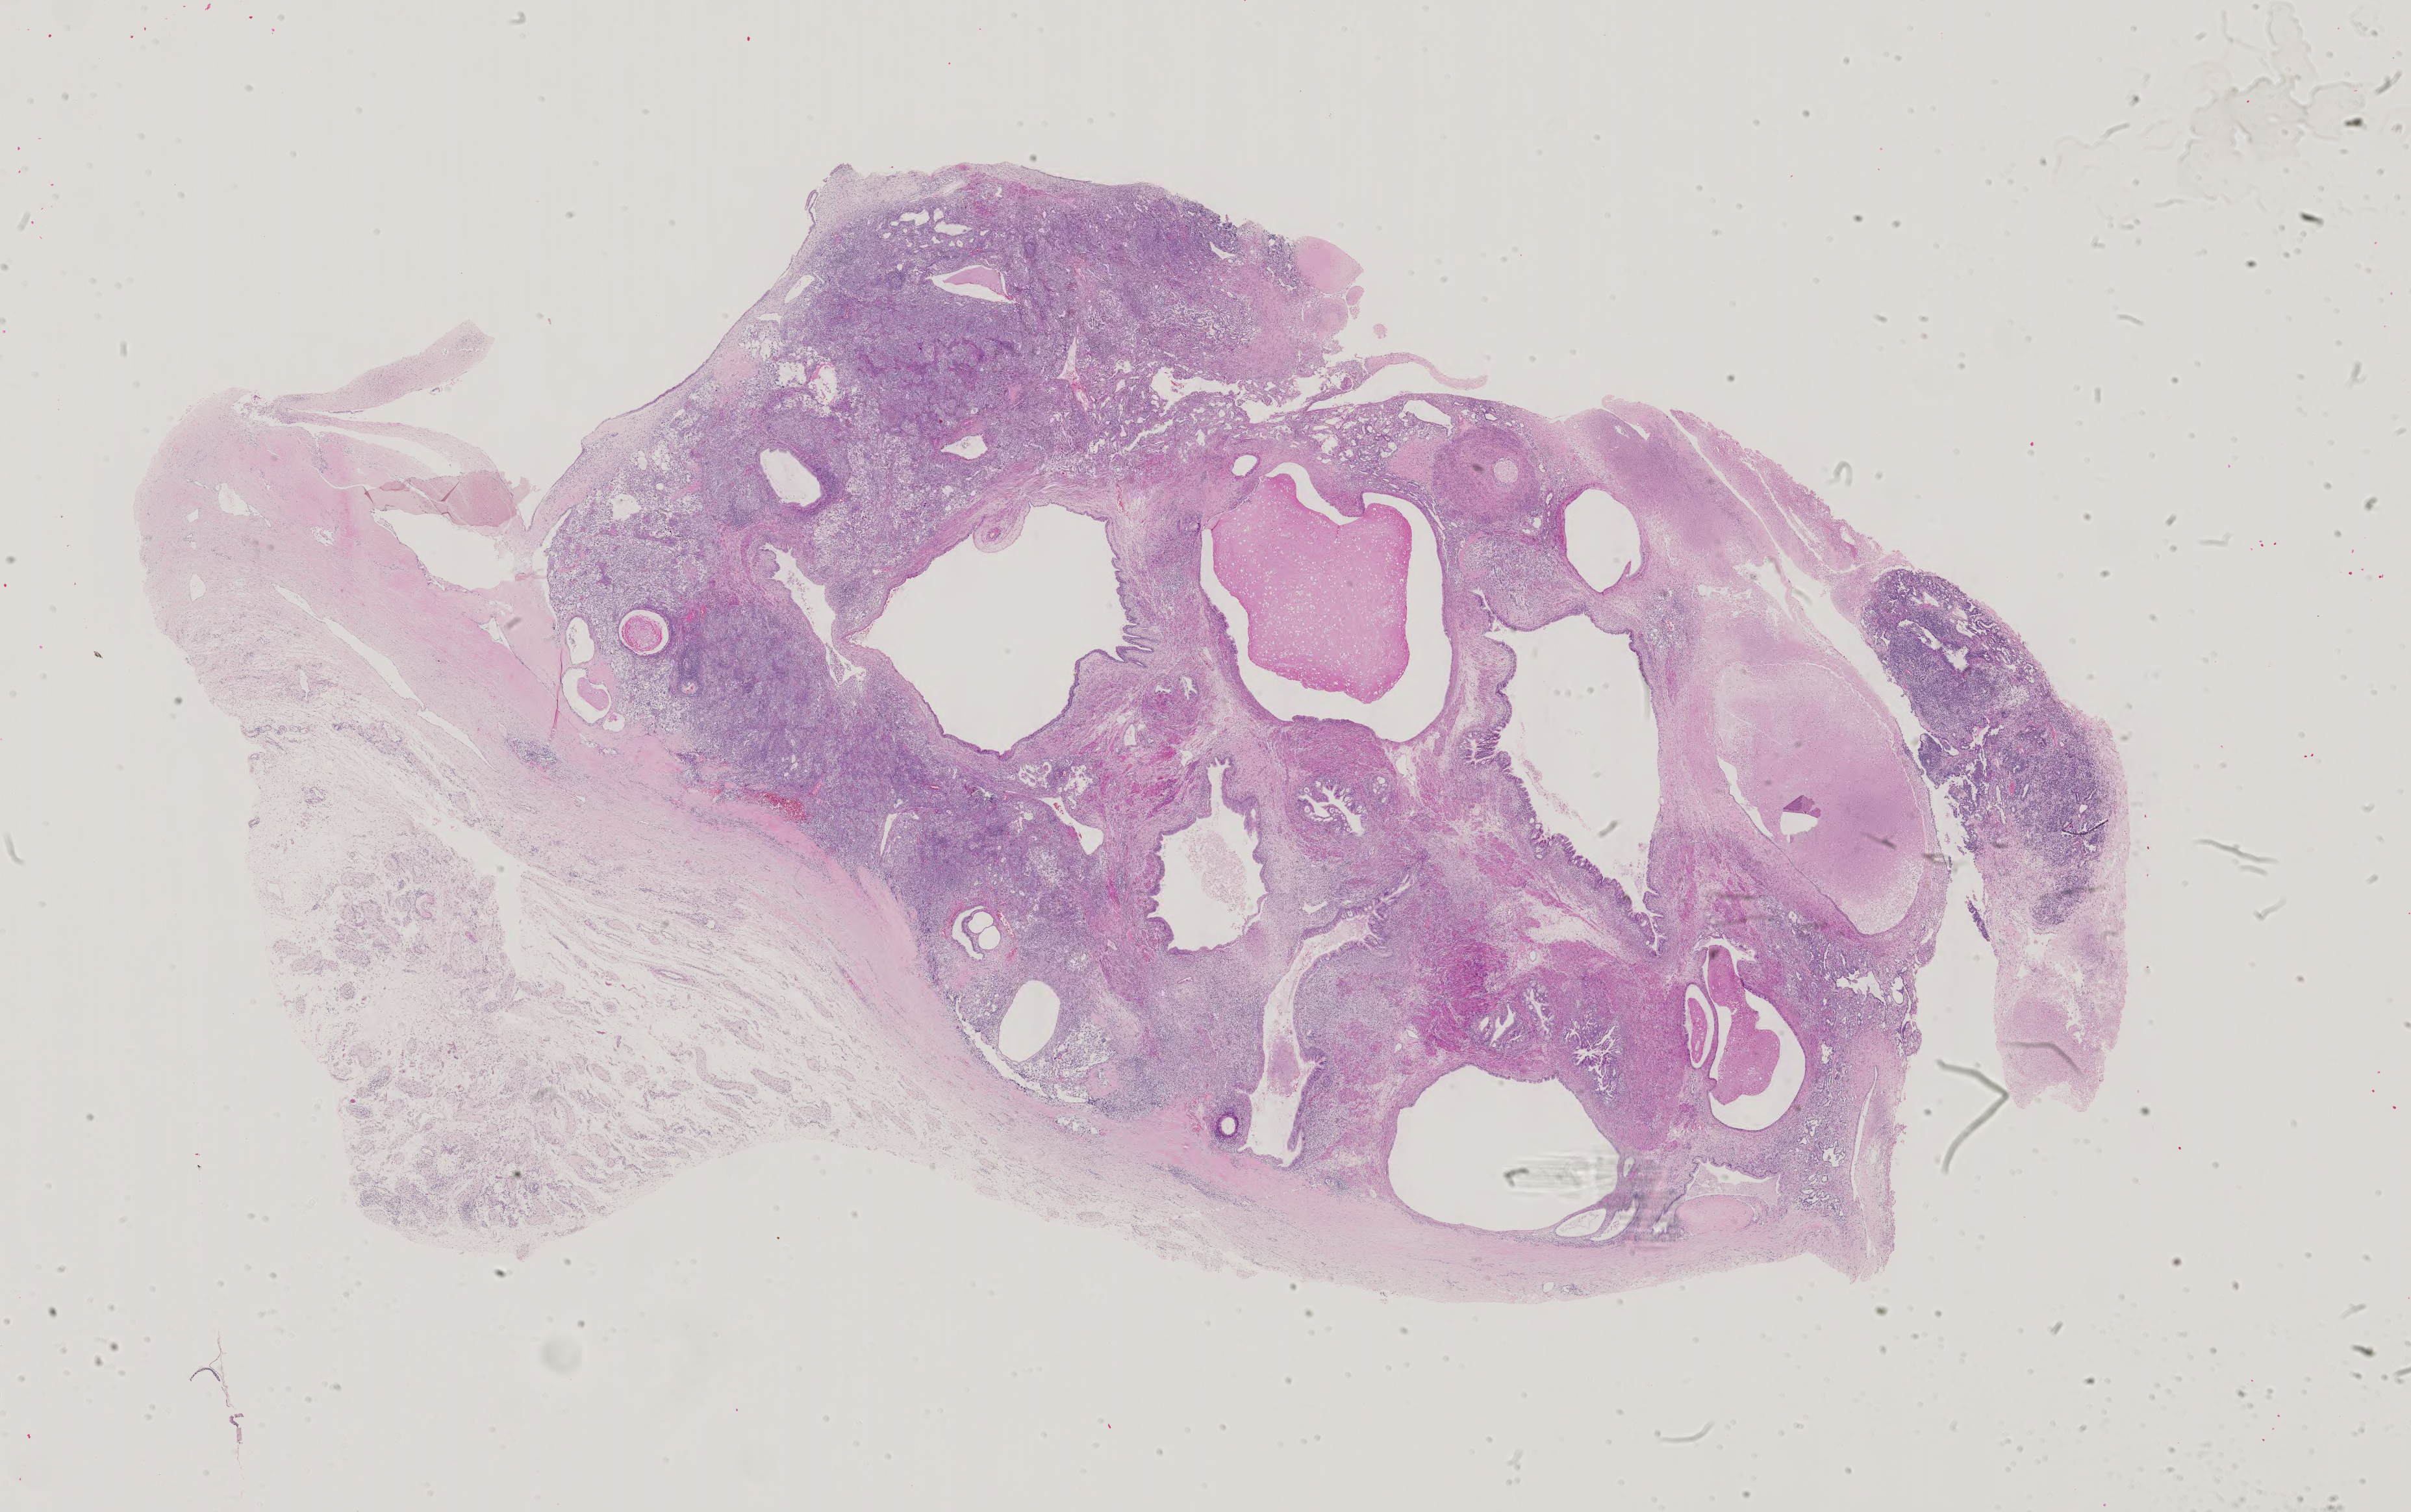
Whole-slide histology image, H&E, shown as a low-resolution overview of the whole scanned area (about 27.0 x 17.0 mm, slide scanned at 40x). Male patient.
- specimen: formalin-fixed paraffin-embedded (FFPE) diagnostic section; testis, primary tumour sample